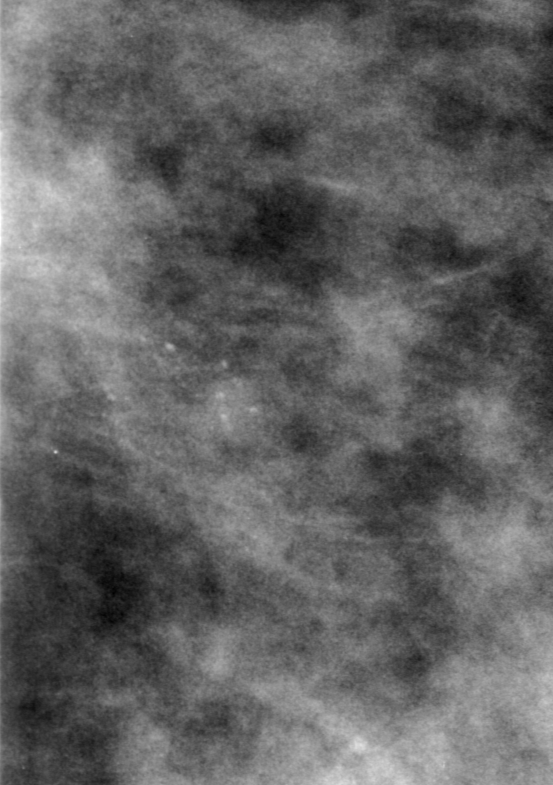
Crop from a digitized film mammogram around one marked abnormality; left breast; CC view; BI-RADS breast density category 3 (scale 1–4).
Calcifications, morphology amorphous, distribution clustered; BI-RADS assessment category 3; subtlety rating 2 on a 1 (subtle) to 5 (obvious) scale; pathology result (as recorded, not read from the image): malignant.